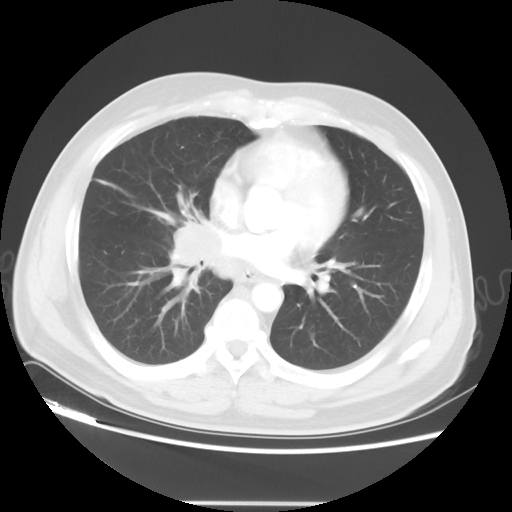
Chest CT, one axial slice; reconstruction kernel STANDARD; 120 kVp; lung window (W 1500 / L -600 HU); 512 × 512 image matrix, field of view 390 × 390 mm. Male patient, age 53 years. Case-level facts recorded for this patient, not image findings: clinical TNM (as recorded): T2 N3 M0; histopathological grade: G3.
Annotated regions visible in this slice (bounding box drawn by a radiologist):
- lung tumour (recorded histology: small cell carcinoma): bounding box (x1, y1, x2, y2) in pixels: (160, 212, 229, 298)